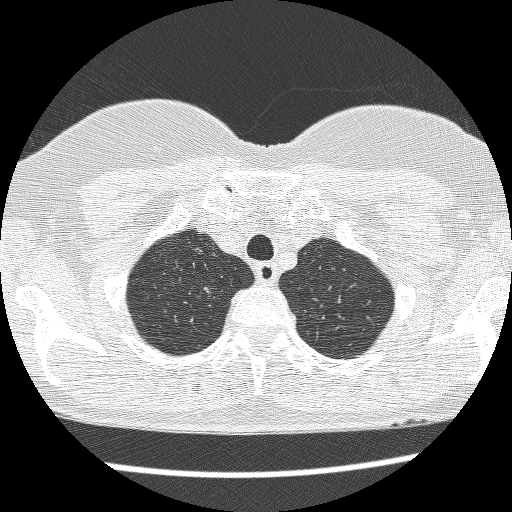
Chest CT (low-dose screening protocol), one axial image; first (baseline) screen; lung window (W 1500 / L -600 HU); lung (sharp) reconstruction kernel (BONE). Female, age 61 years at enrolment.
Expert reader's lesion annotation, bounding box (x1, y1, x2, y2) in pixels: (188, 278, 232, 308). Reader record for this screening exam (exam-level; its link to the box is not recorded): non-calcified nodule or mass ≥4 mm, right upper lobe, 7 × 6 mm, poorly defined margins, mixed attenuation. Later outcome: lung cancer diagnosed 403 days after this screen — adenocarcinoma, NOS, right upper lobe, poorly differentiated (G3), 12 mm at pathology.